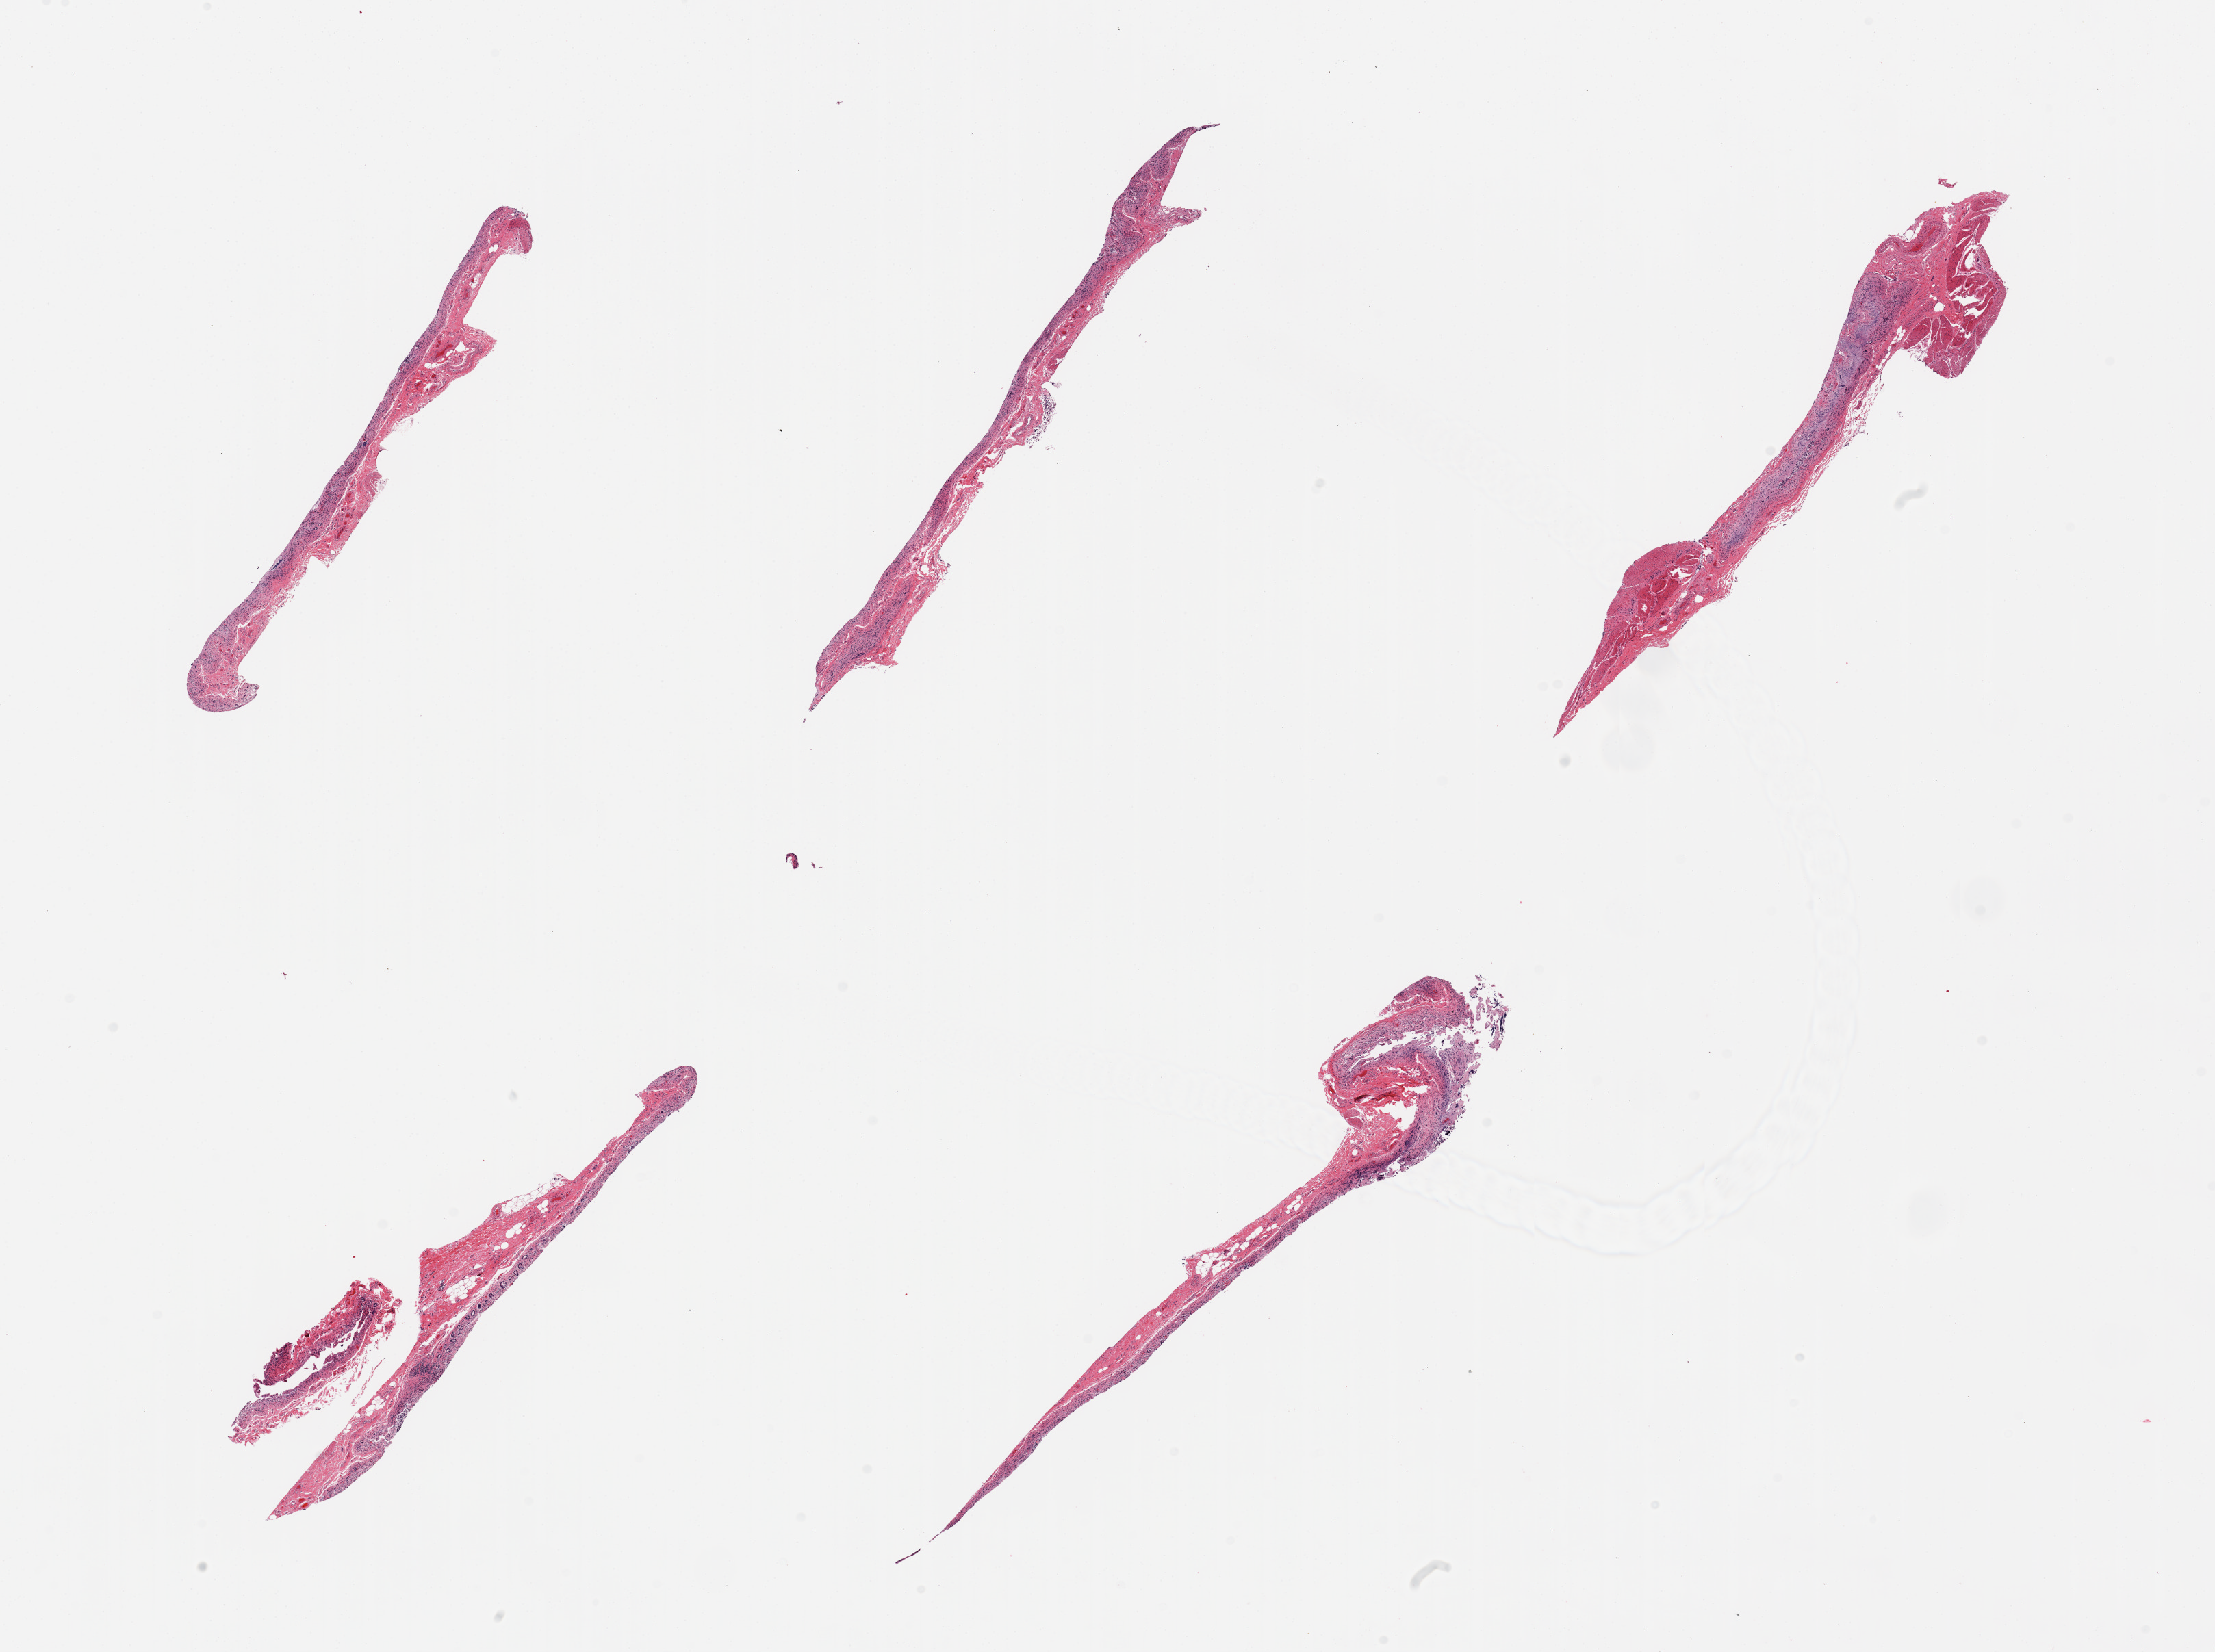
Hematoxylin and eosin (H&E) whole-slide image — low-resolution overview of the scanned area, about 25.6 x 19.1 mm, PAXgene-fixed, paraffin-embedded tissue, sampled site (target tissue): ileum, tissue donor sample. Donor sex: male.
Review note (as recorded): 6 pieces; autolyzed mucosa, no lymphoid nodules present, small foci of muscularis (not target).